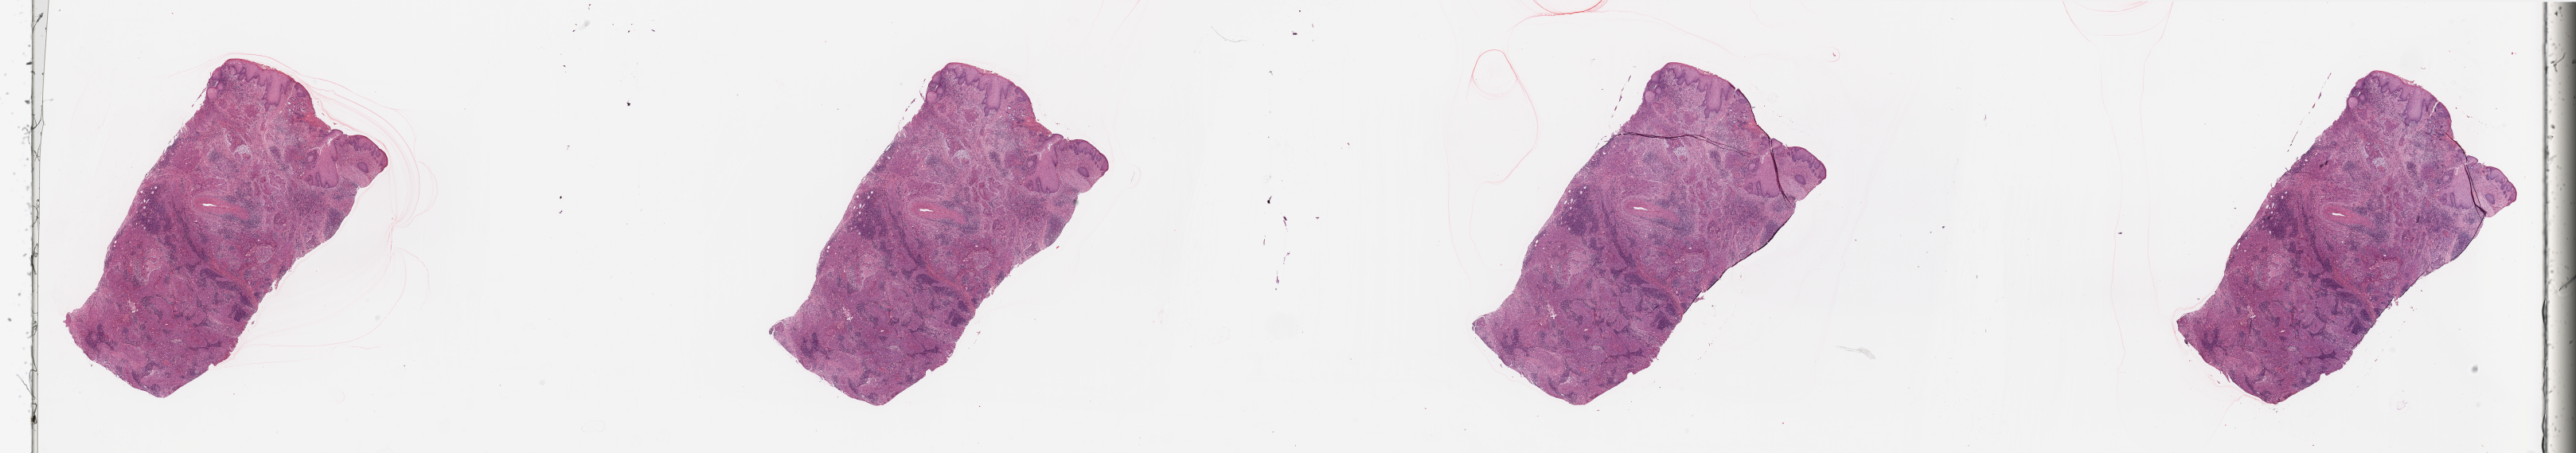
Digitized H&E tissue section (whole slide) — shown as a low-resolution overview of the whole scanned area (about 51.2 x 9.0 mm, acquisition: 20x scan); tumour tissue sample, sampled site: larynx. Male, 68 y/o. Histologic grade: G3 (poorly differentiated). Slide review estimates, as recorded: tumour nuclei 80%, necrosis 5%.
Diagnosis: Squamous cell carcinoma, NOS (larynx, NOS). AJCC pathologic stage: I.